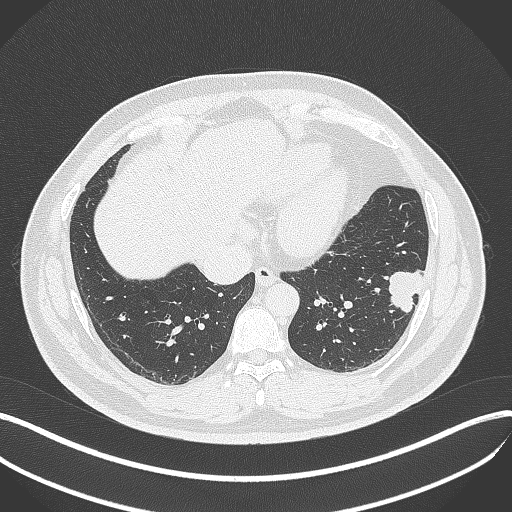
Chest CT, one axial slice. Lung window (W 1500 / L -600 HU). 1 mm slice thickness. 512 × 512 image matrix, field of view 400 × 400 mm. Patient: male, 39 years. From the clinical record (not read from this slice): clinical TNM (as recorded): T2a N0 M0; histopathological grade: G2-3.
Annotated regions visible in this slice (bounding box drawn by a radiologist):
- lung tumour (recorded histology: adenocarcinoma): bounding box (x1, y1, x2, y2) in pixels: (380, 264, 431, 318)